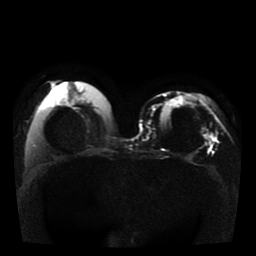
Breast MRI, one axial slice; slice 16 of 41 in the series (ordered by position); diffusion-weighted series; image 2 of 4 stored at this slice position (different b-values; order by instance number); 1.5 T; 5 mm slice thickness; 256 × 256 image matrix, field of view 330 × 330 mm. Female patient.
Outlined on this slice (outlined manually by an expert reader):
- tumour on diffusion-weighted imaging: box from (x=205, y=135) to (x=213, y=140) px